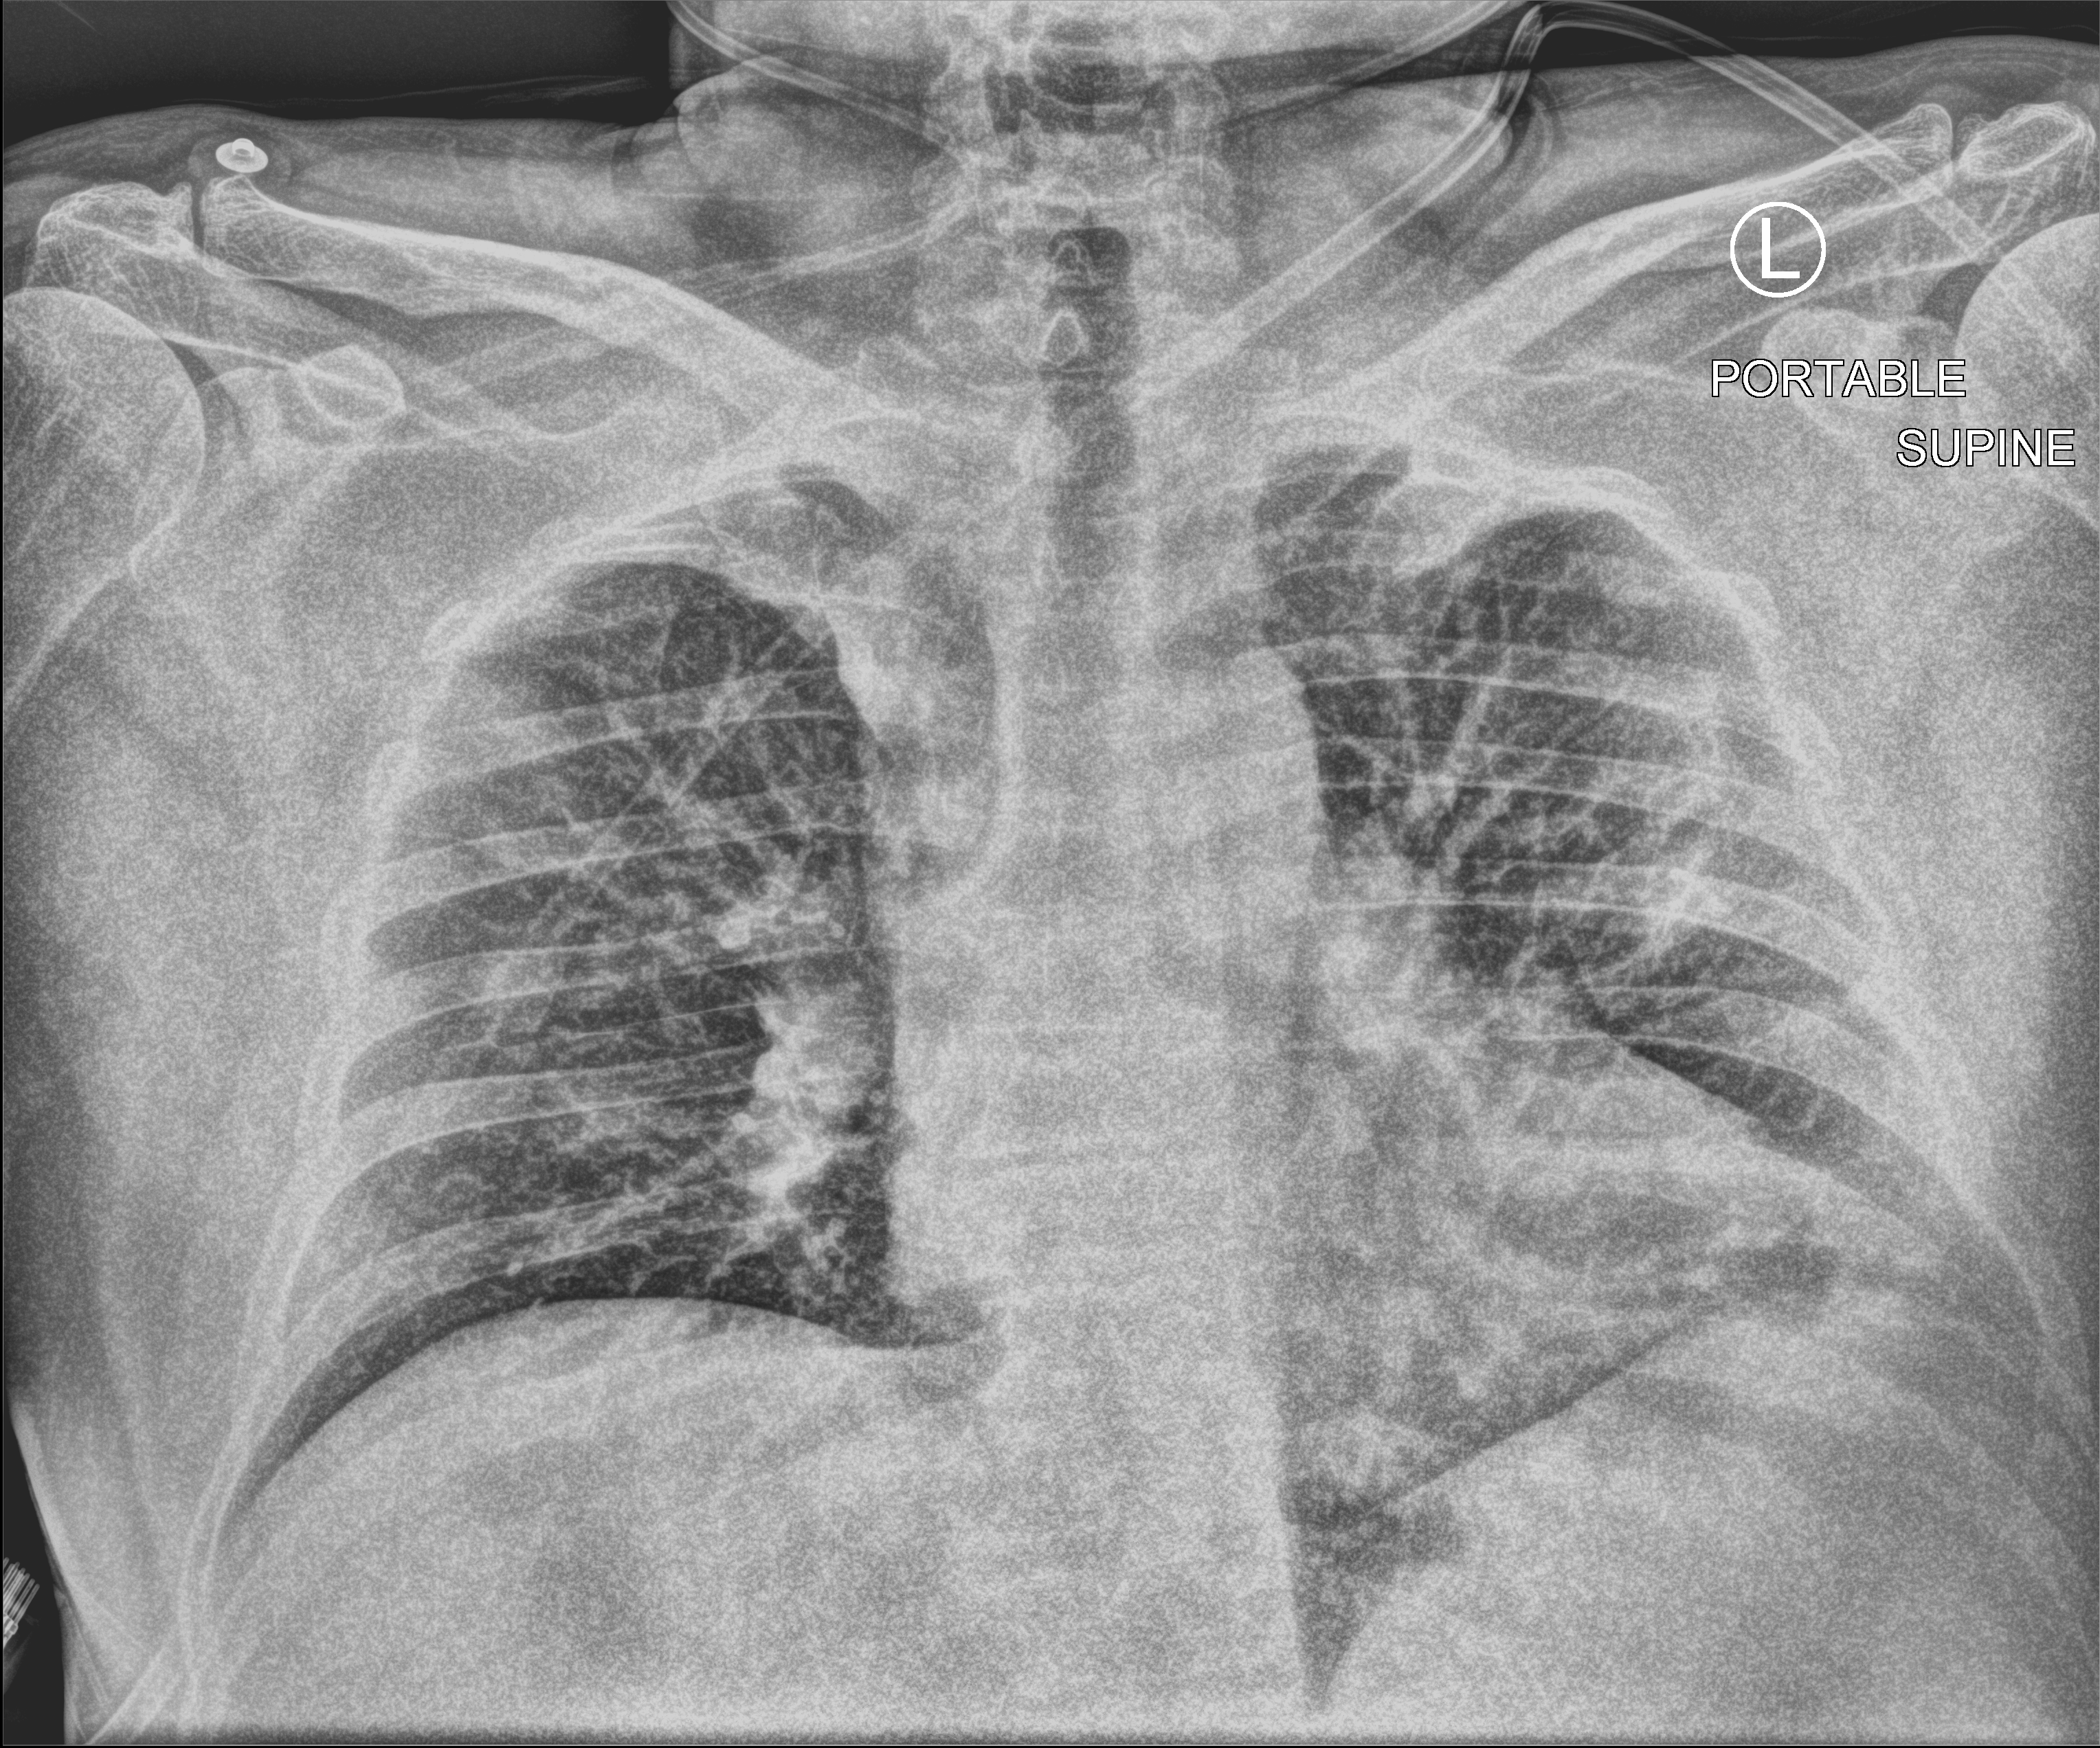
Portable chest radiograph; anteroposterior (AP) projection. Patient hospitalised with COVID-19; male, aged 60–74 years.
Admission-level facts for this patient (not findings on this image; timing relative to this image not recorded): mechanically ventilated during this hospital stay: no.